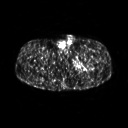
FDG PET of an extremity soft-tissue mass (from a PET/CT study), one axial slice; slice 262 of 267 in the series (ordered by position); 3.27 mm slice thickness; 128 × 128 image matrix, field of view 500 × 500 mm. Male patient, age 27 years. From the clinical record (not read from this slice): histological type: extraskeletal osteosarcoma; grade: high; site of the primary tumour: left adductur.
Structures marked on this image (expert contour drawn on MRI and transferred to this co-registered scan by the dataset authors):
- gross tumour volume (mass): bounding box (x1, y1, x2, y2) in pixels: (71, 50, 97, 75)